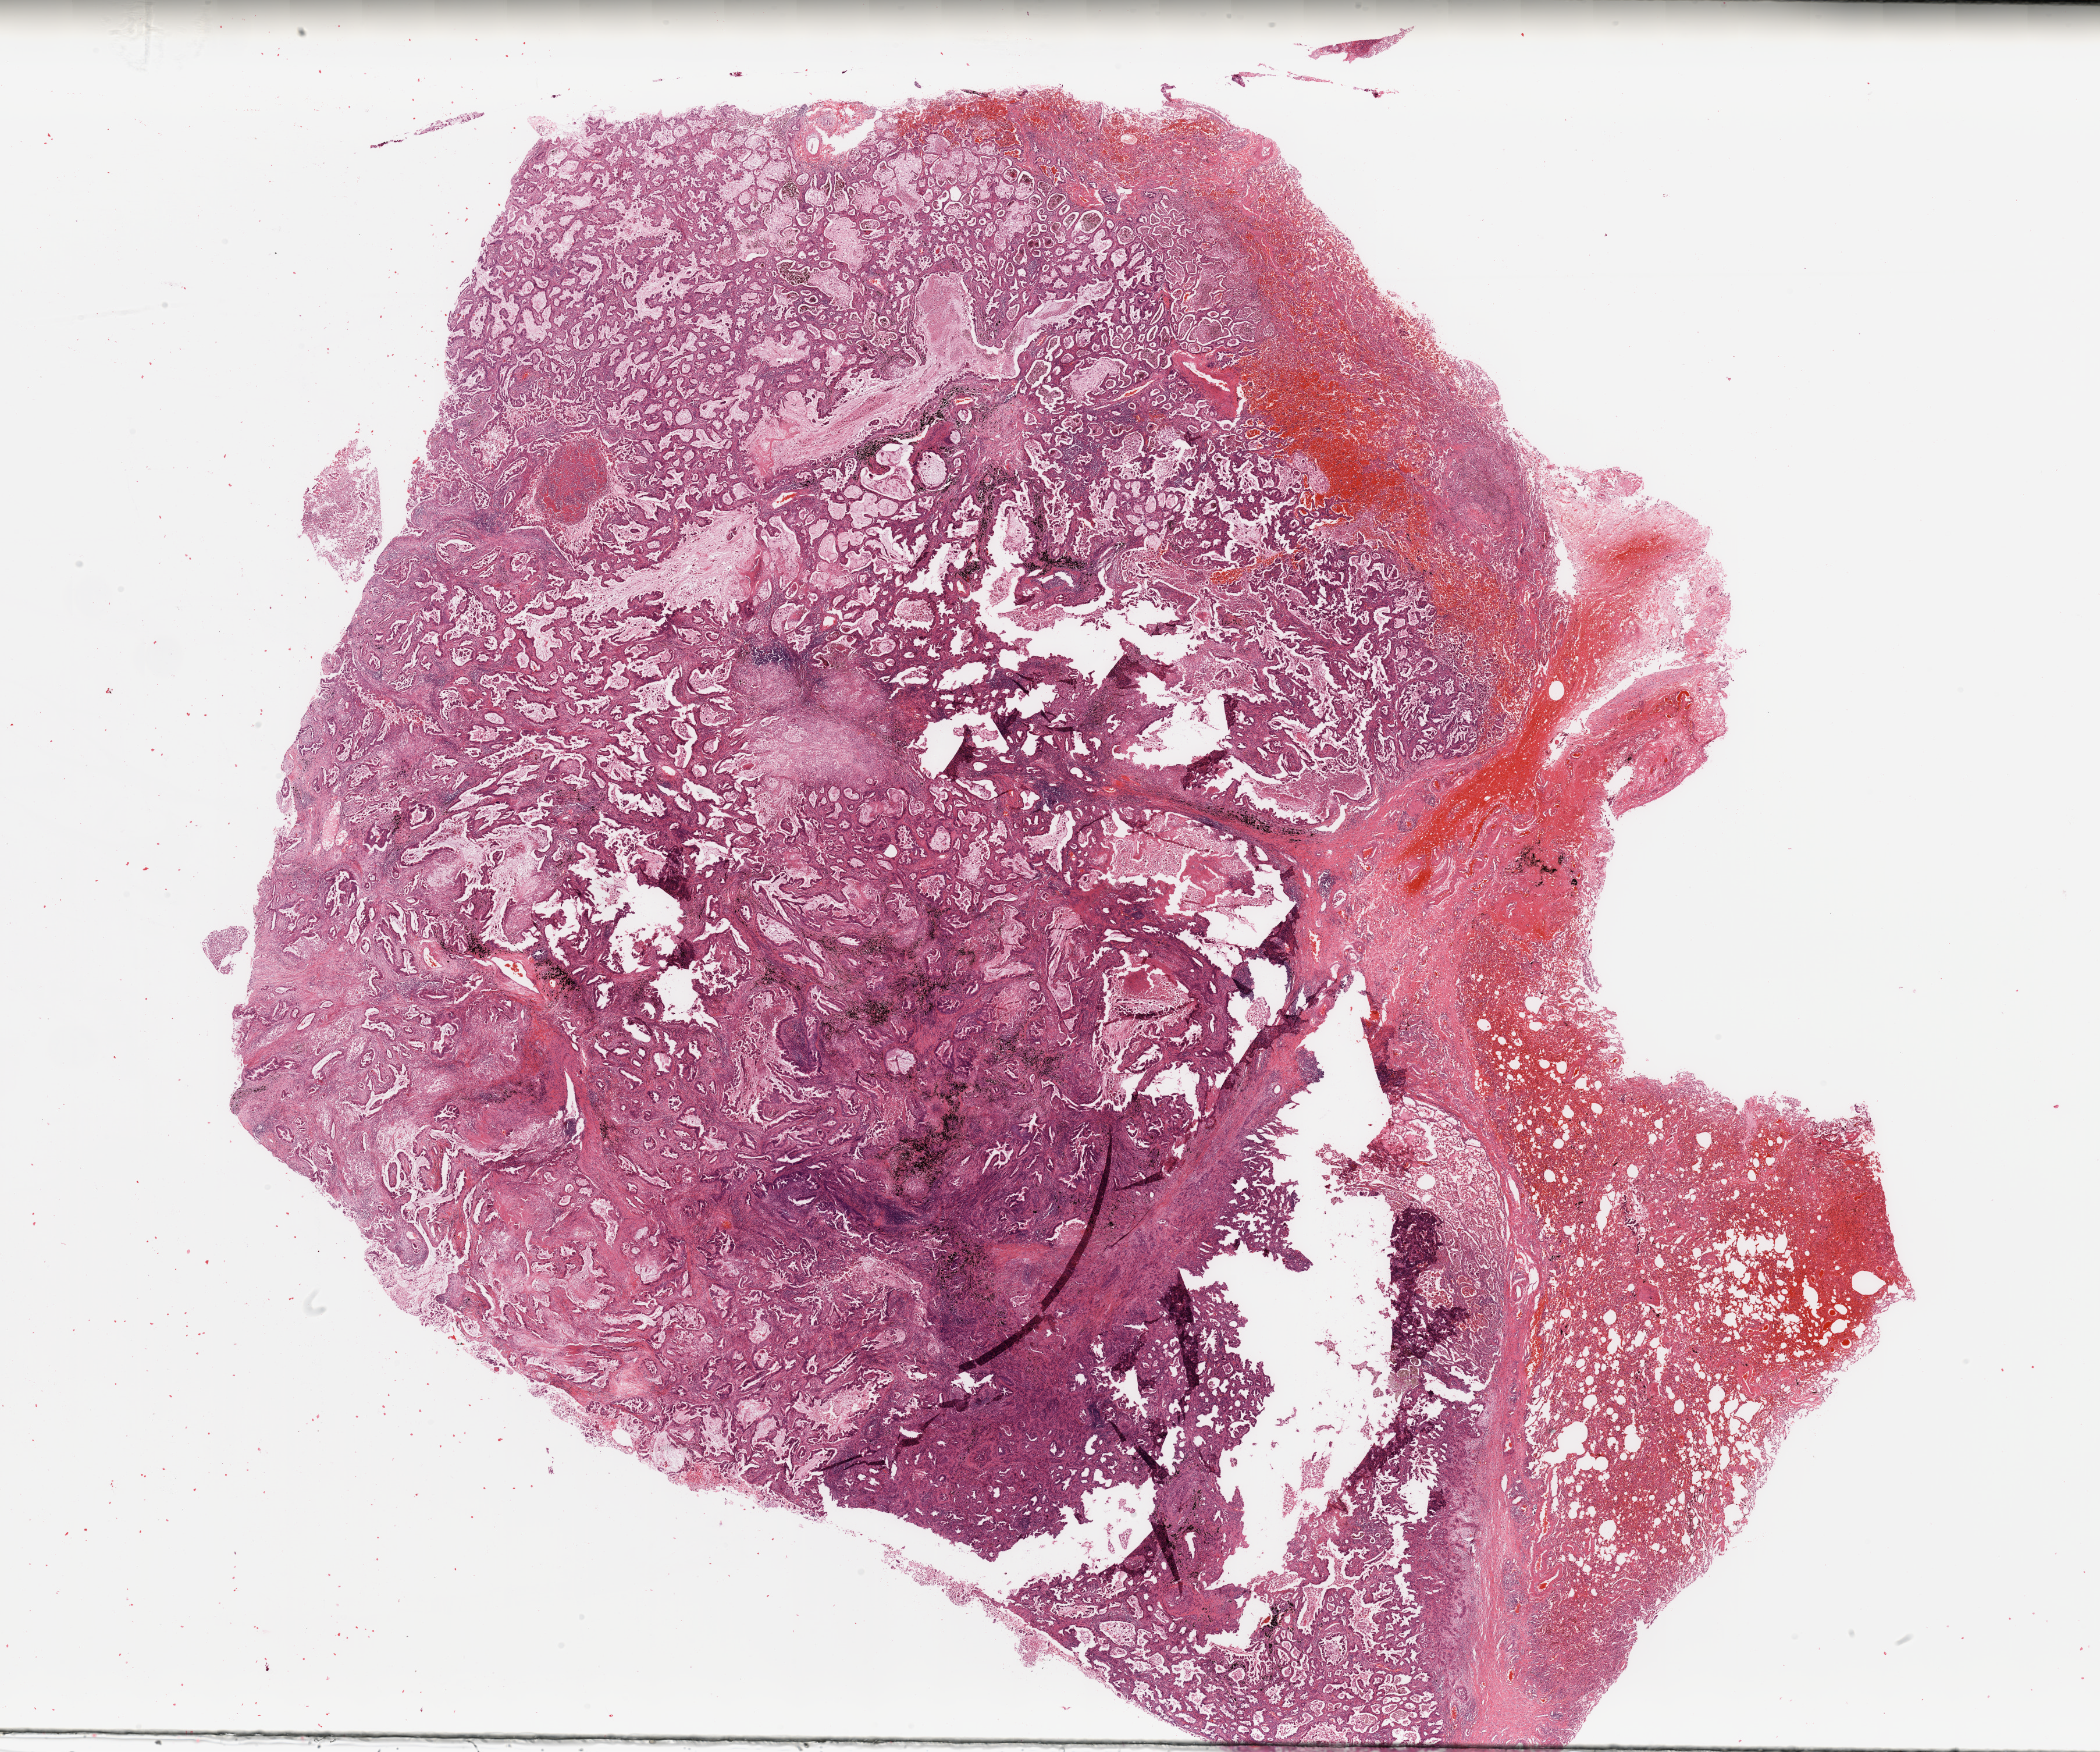
H&E-stained whole-slide image — shown as a low-resolution overview of the whole scanned area (about 28.5 x 23.8 mm), lung, tumour tissue. 58-year-old male patient. Histologic grade: G2 (moderately differentiated).
AJCC pathologic stage: IIIA. Histologic diagnosis: Adenocarcinoma, NOS.